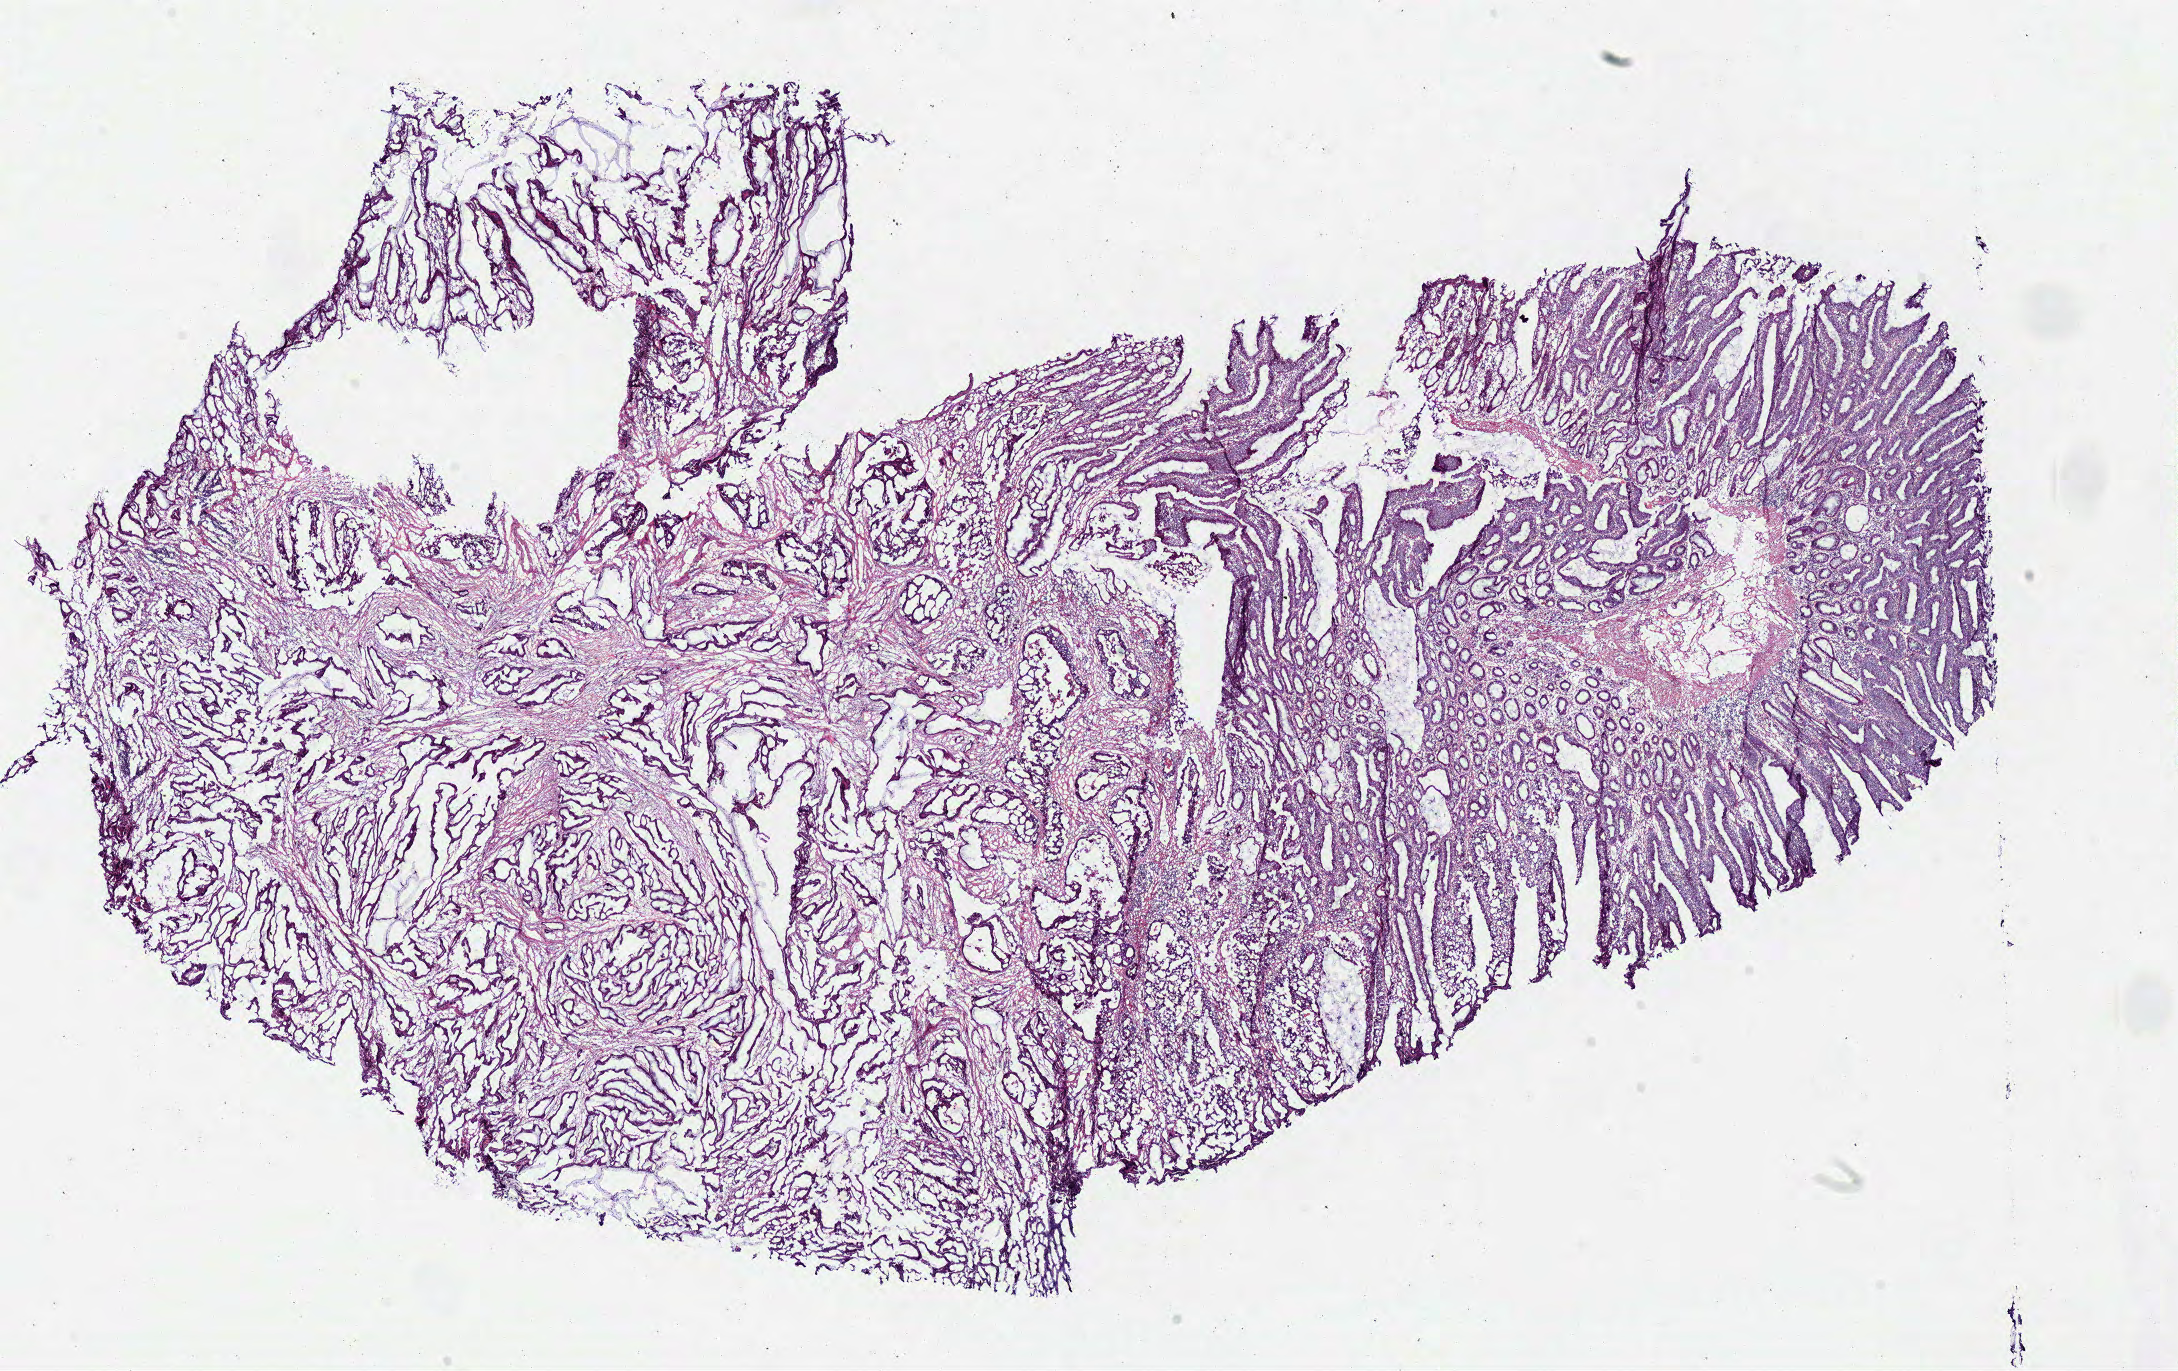
Whole-slide histology image, Hematoxylin and eosin (H&E) stained, shown as a low-resolution overview of the whole scanned area (about 17.1 x 10.8 mm, from a 40x scan). Frozen section from the bottom of the tissue portion. Colon, primary tumour sample. Patient: male, age at initial diagnosis 73 years. Slide review estimates, as recorded: tumour cells 67%, tumour nuclei 75%, normal cells 15%, stromal cells 10%, necrosis 8%.
Lymph nodes positive (case pathology): 2 of 65 examined. Pathologic diagnosis: Adenocarcinoma, NOS. AJCC pathologic stage: III (6th edition). TNM: T3 N1 MX.